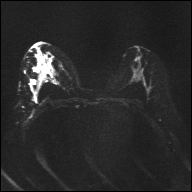
Breast MRI, one axial slice; position 15 of 32 along the scan axis; diffusion-weighted series; image 2 of 4 stored at this slice position (different b-values; order by instance number); 1.5 T; 4 mm slice thickness; 192 × 192 image matrix, field of view 360 × 360 mm. Female patient.
Outlined on this slice (expert manual segmentation):
- tumour on diffusion-weighted imaging: box from (x=39, y=61) to (x=41, y=66) px